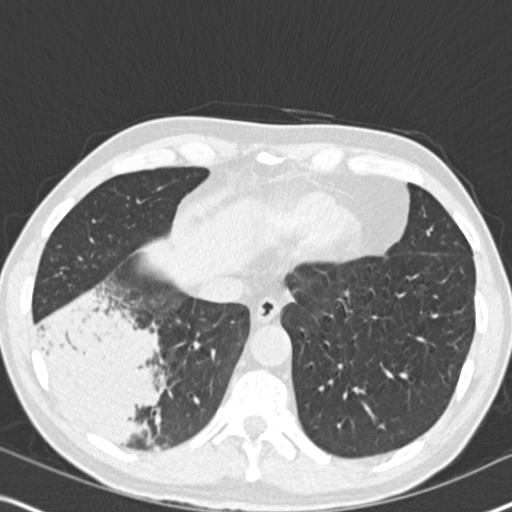
Low-dose screening chest CT, one axial slice; position 60 of 182 along the scan axis; 120 kVp; lung window (W 1500 / L -600 HU); 2 mm slice thickness; 512 × 512 image matrix, field of view 330 × 330 mm.
Structures marked on this image (expert manual segmentation):
- lesion 1 (tumor, lower lobe of right lung): bounding box <42,299,150,440> (left, top, right, bottom; pixels)